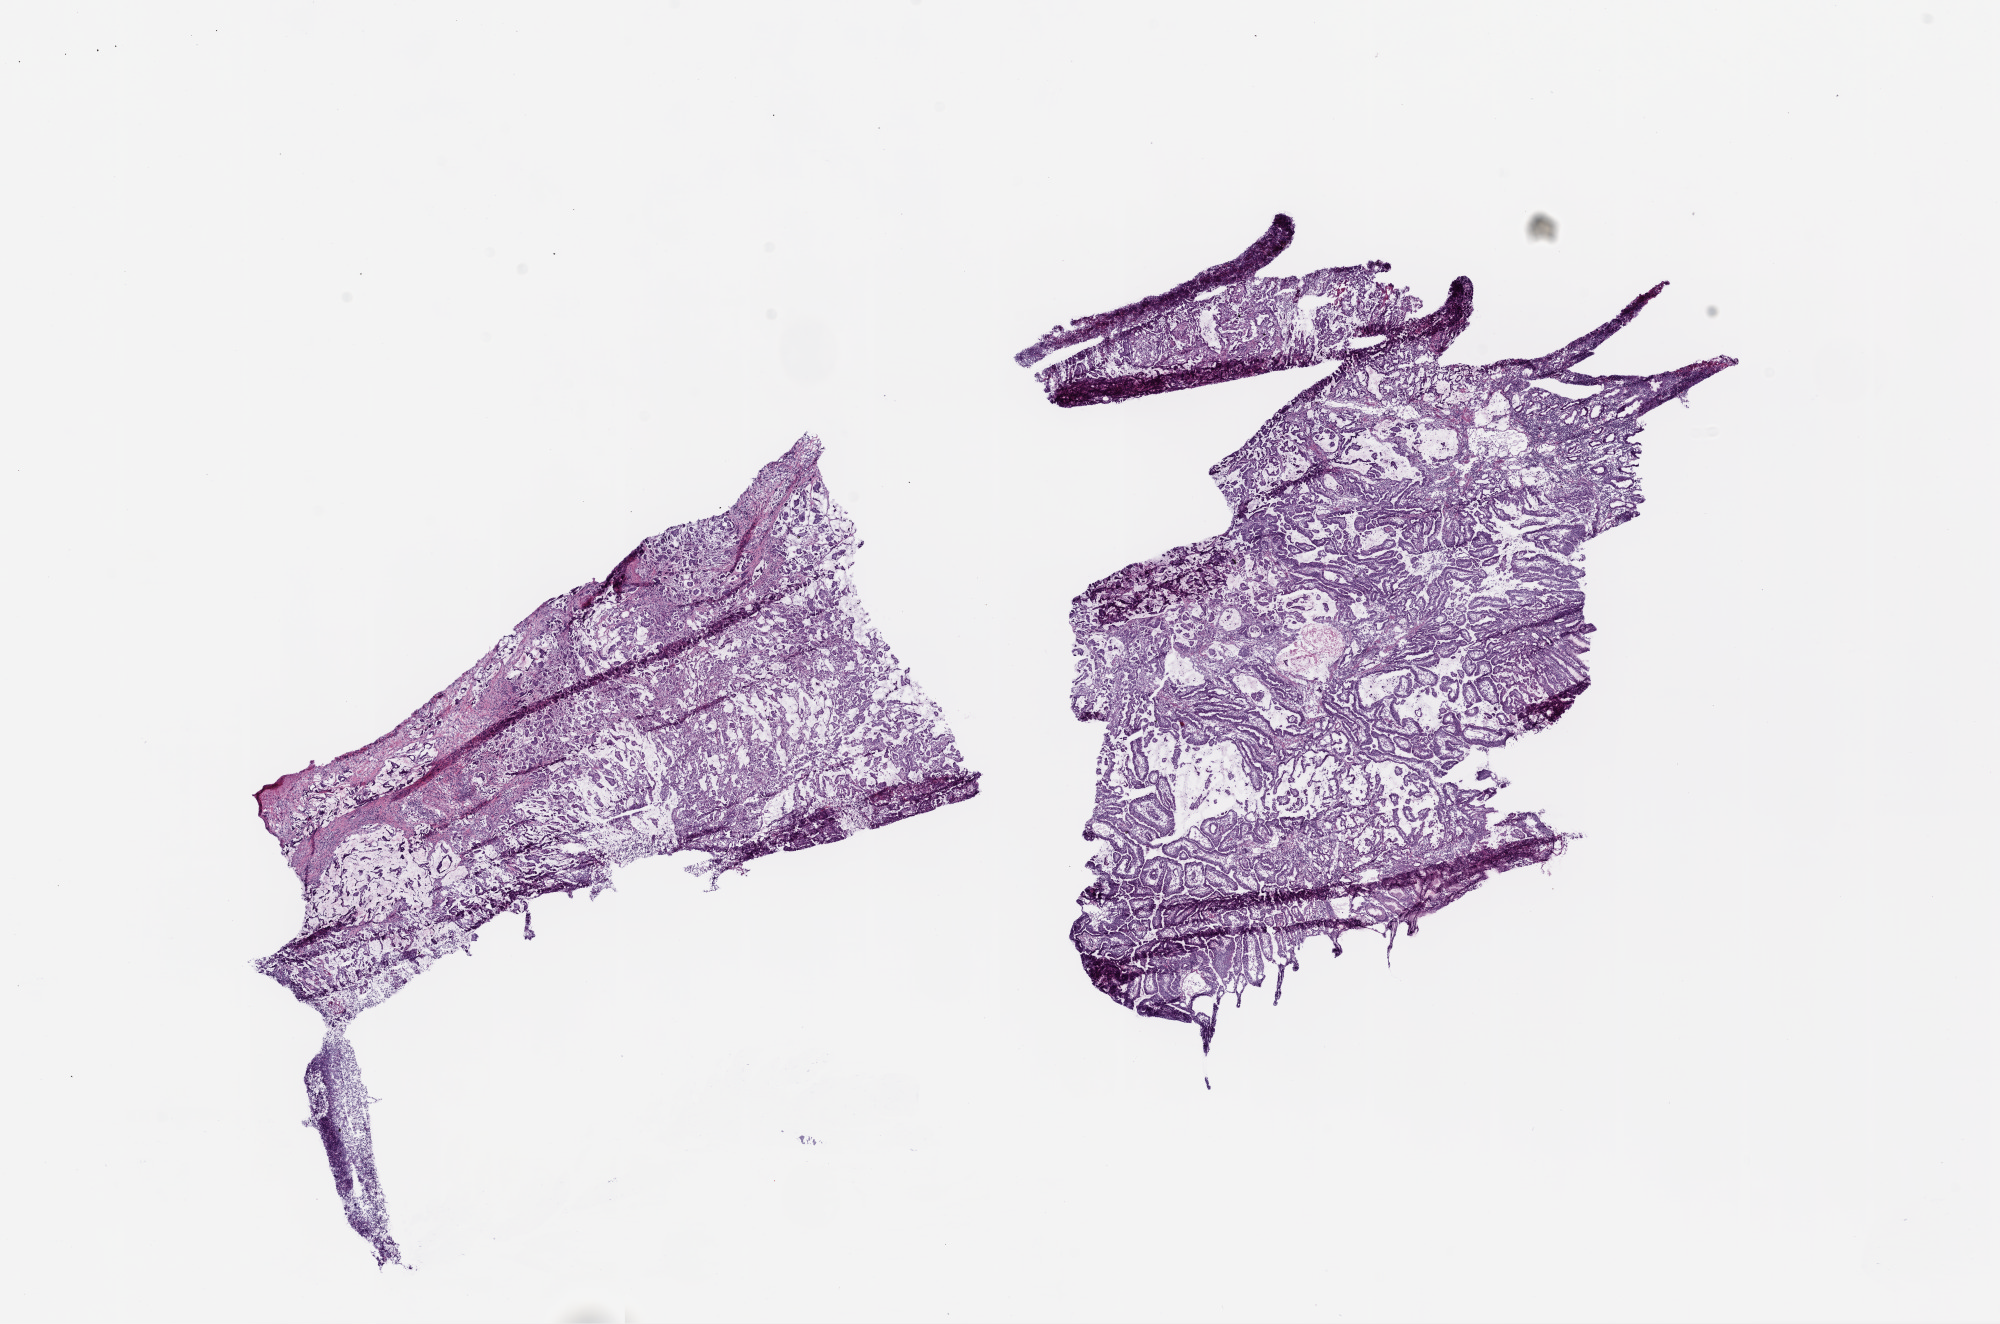
Whole-slide histology image, Hematoxylin and eosin (H&E) stained — a low-resolution overview of the entire scanned area, about 16.0 x 10.6 mm (slide scanned at 20x), frozen section from the top of the tissue portion, stomach, primary tumour sample. Patient sex: male. Histologic grade: G3 (poorly differentiated). Pathologist review of this section (percent, as recorded): tumour cells 99%, tumour nuclei 80%, normal cells 0%, stromal cells 0%, necrosis 1%. Infiltration values recorded for this section: lymphocyte infiltration 10%, monocyte infiltration 0%, neutrophil infiltration 5%.
• AJCC pathologic stage: IV (5th edition)
• diagnosis: Adenocarcinoma, NOS (gastric antrum)